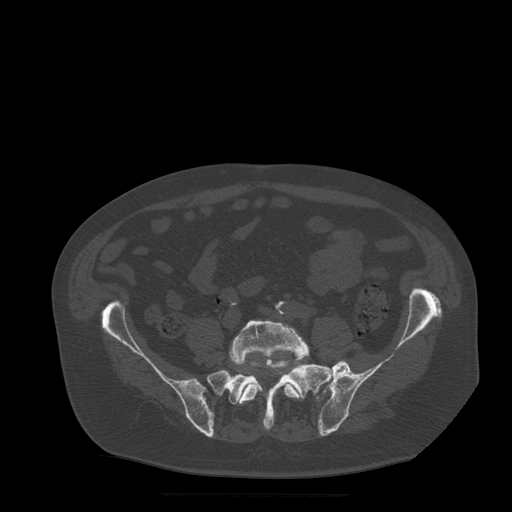
CT including the spine, one axial slice. Position 78 of 522 along the scan axis. Bone window (W 1800 / L 400 HU). 1.25 mm slice thickness. 512 × 512 image matrix. Patient age 72 years. Case-level facts recorded for this patient, not image findings: primary cancer: prostate.
Annotated regions visible in this slice (semi-automatically segmented with operator editing):
- L5 vertebra: bounding box <231,321,310,404> (left, top, right, bottom; pixels)